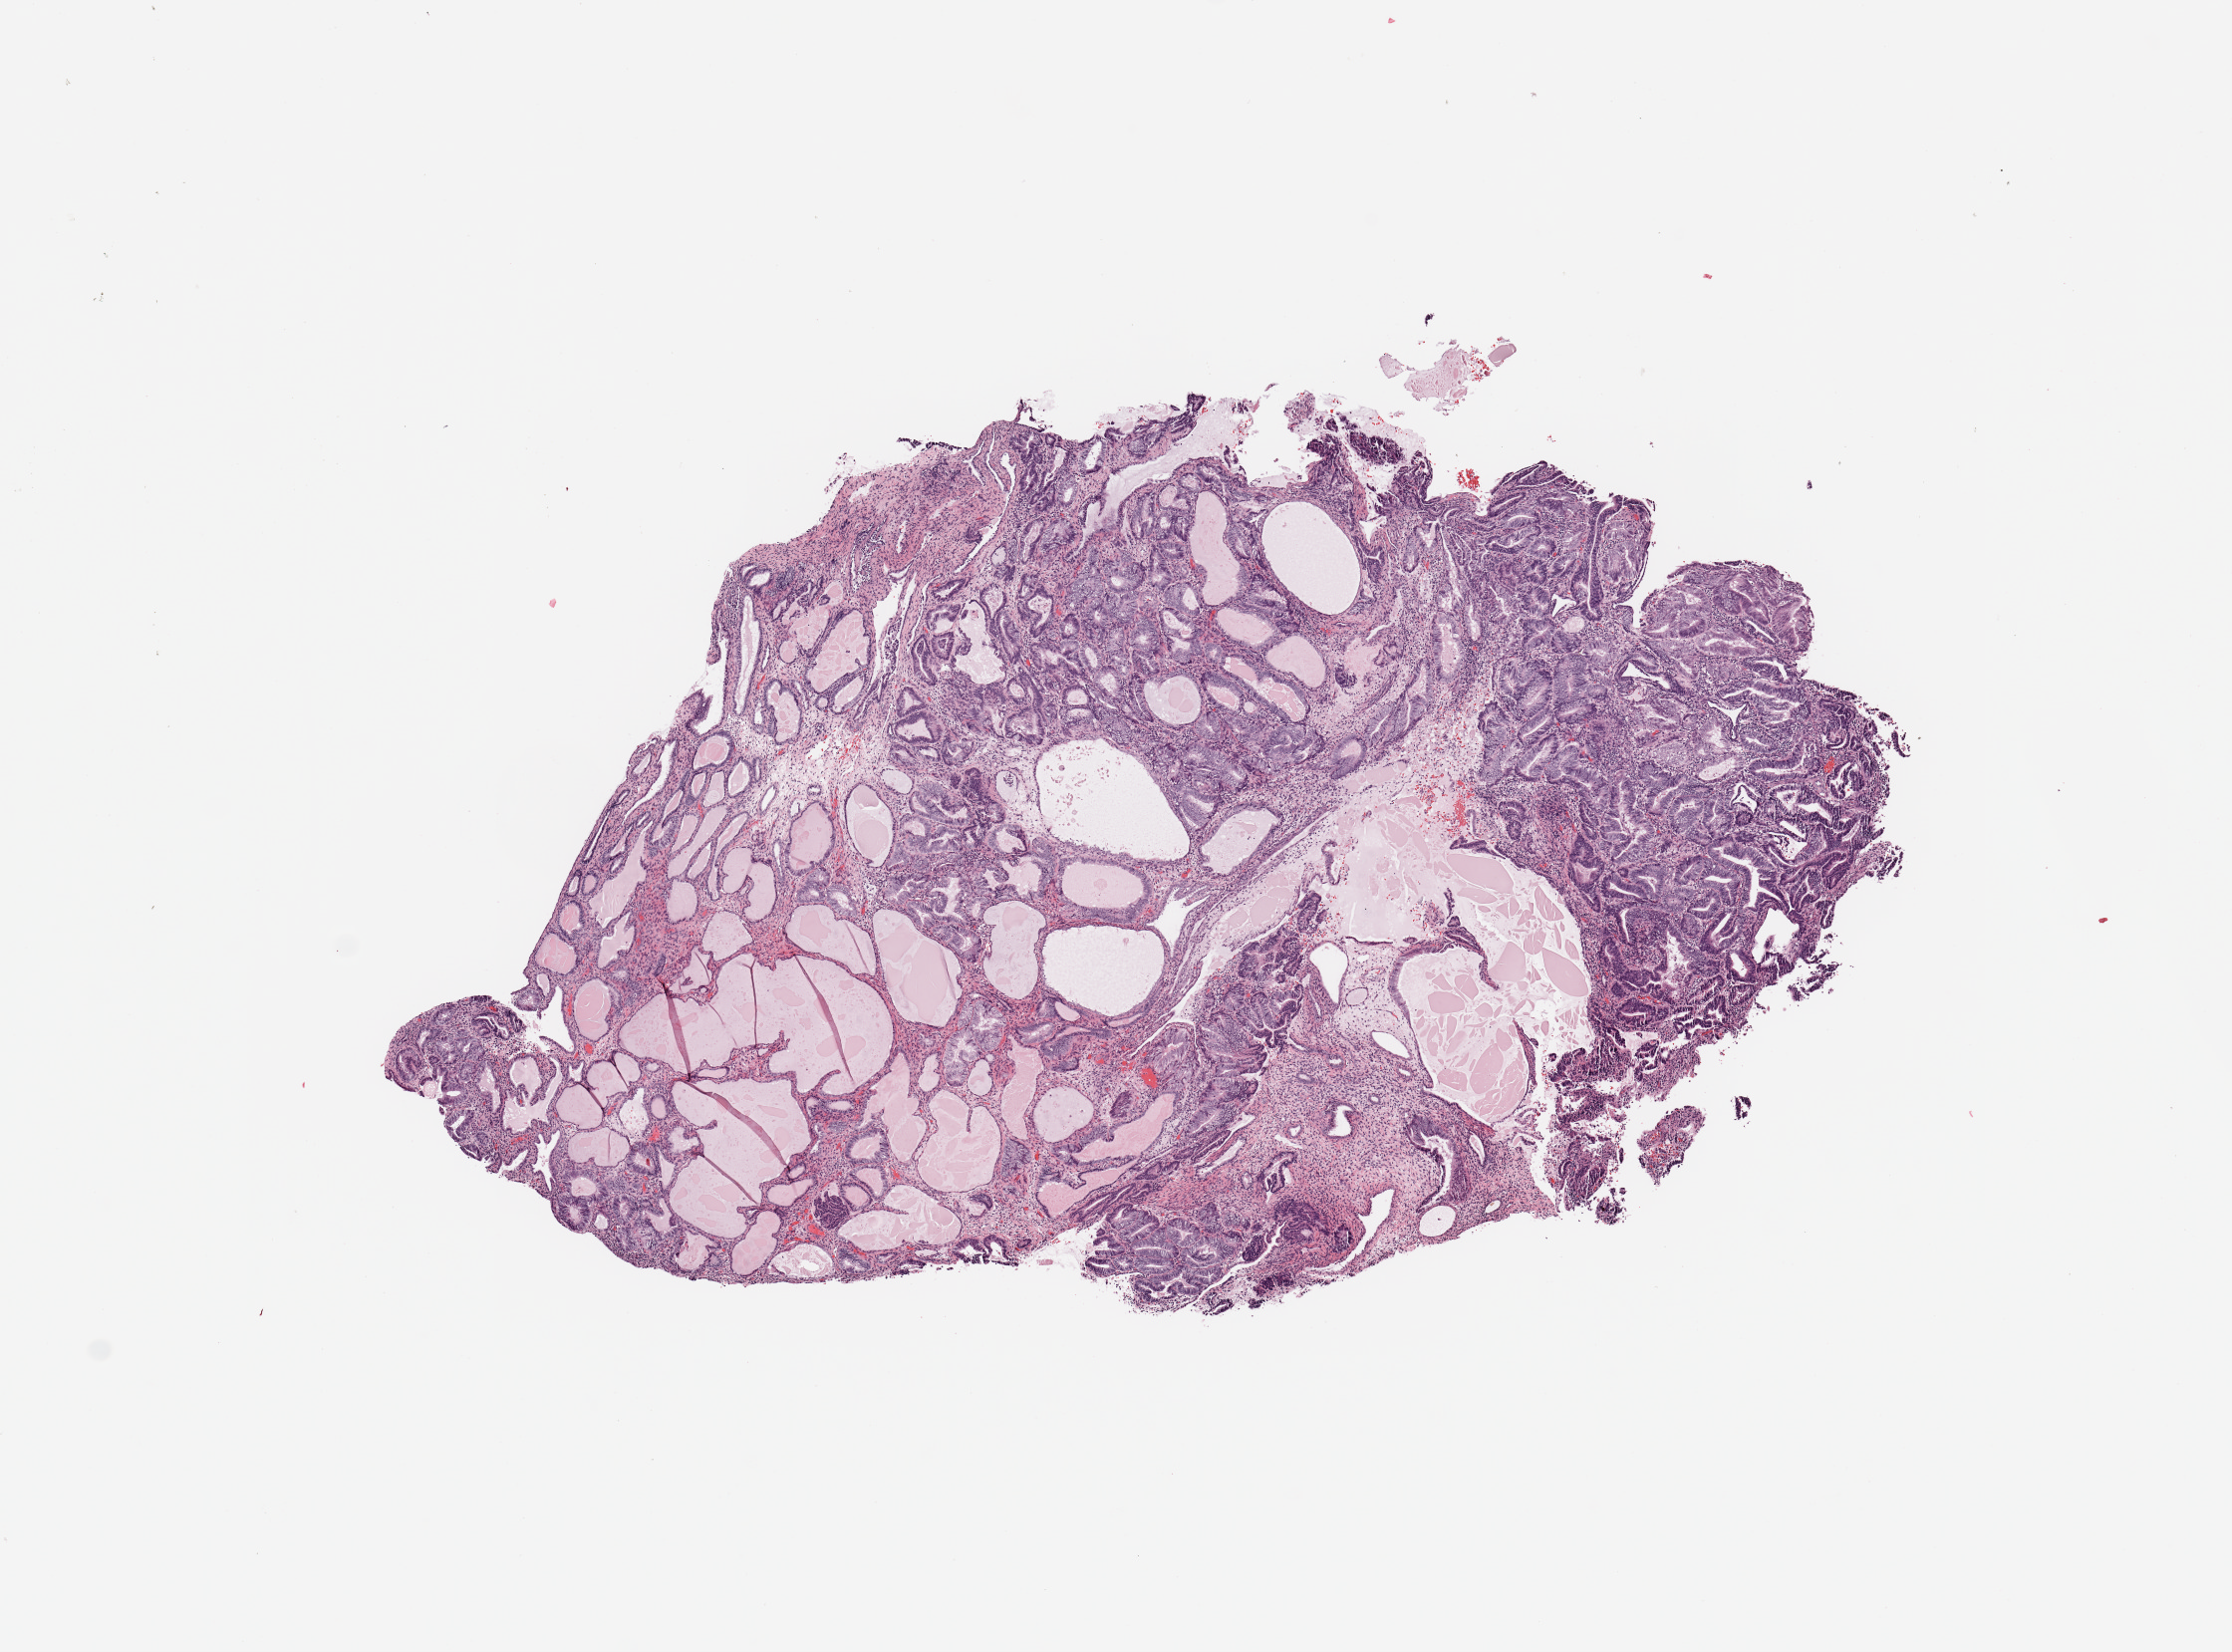
Whole-slide histology image, Hematoxylin and eosin (H&E) stained — shown as a low-resolution overview of the whole scanned area (about 8.9 x 6.6 mm, slide scanned at 20x); tumour tissue sample, sampled site: uterus. 64-year-old female patient. Histologic grade: G1 (well differentiated). Slide review estimates, as recorded: tumour nuclei 80%, necrosis 0%.
AJCC pathologic stage: I. Primary tumour site (as recorded): anterior endometrium. Diagnosis: Endometrioid adenocarcinoma, NOS.